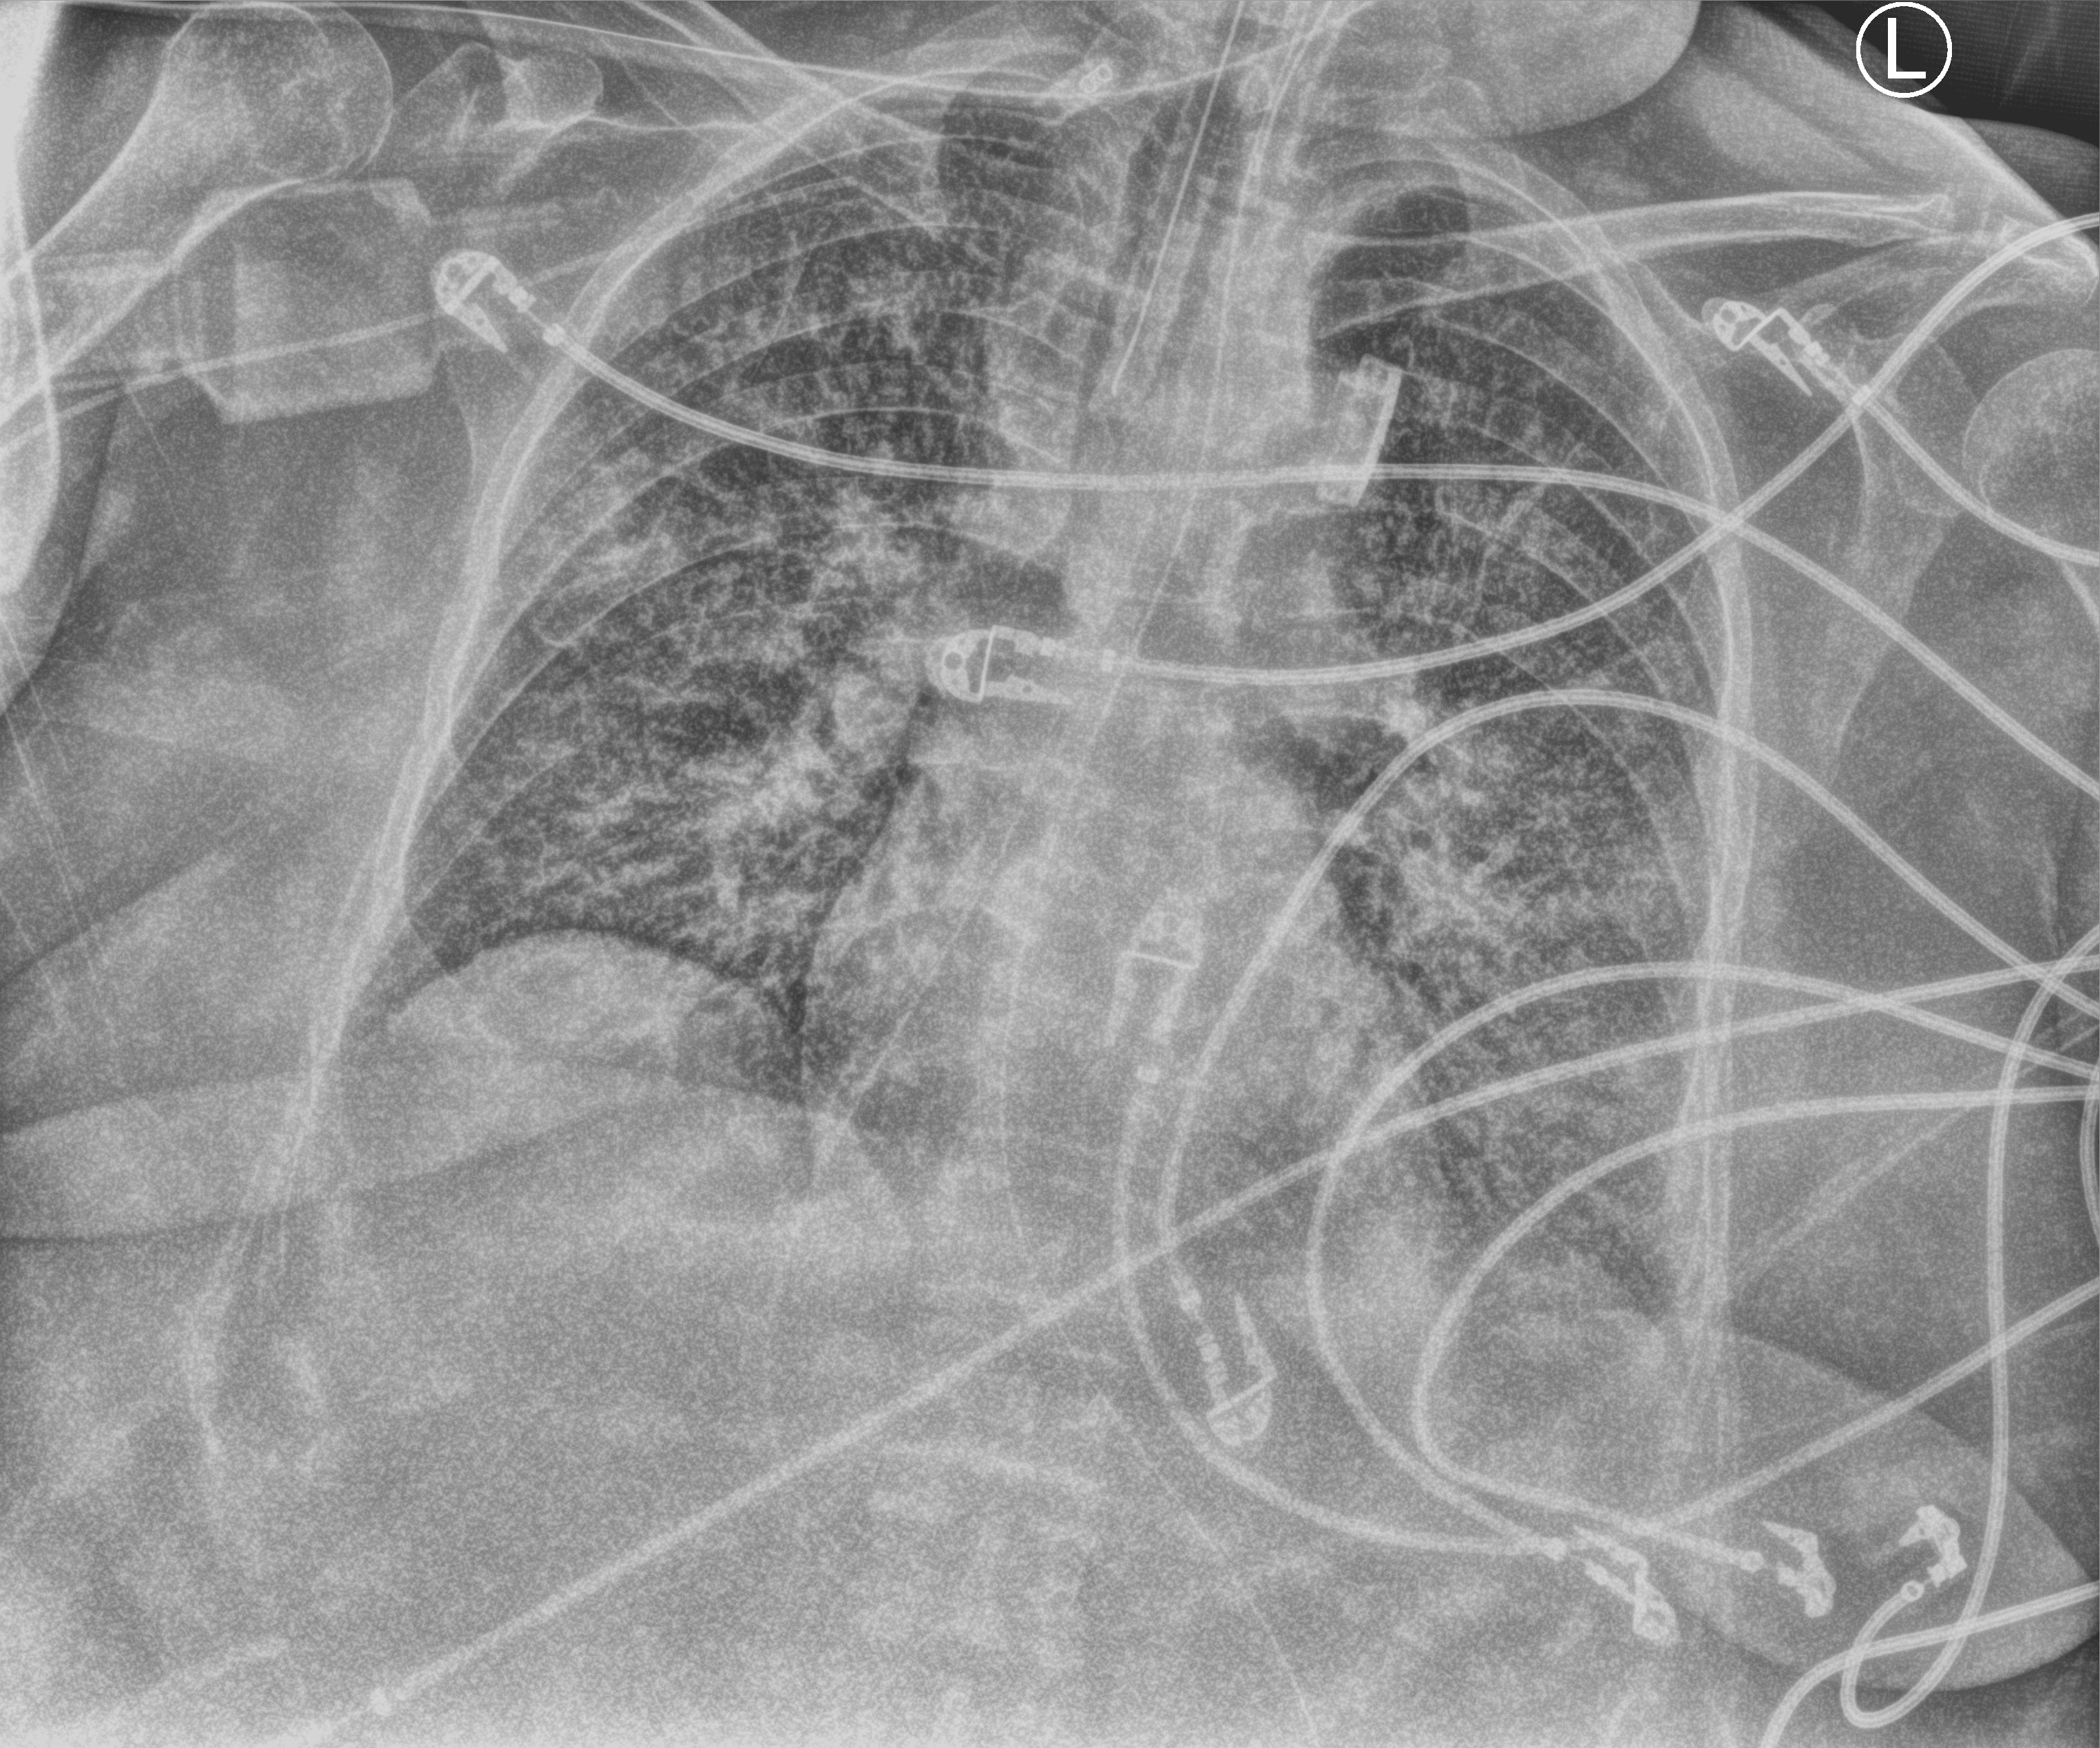
Chest X-ray (portable); anteroposterior (AP) projection. Patient hospitalised with COVID-19; female, aged 60–74 years.
From the hospital-stay record, not from the radiograph (when in the stay this image was taken is not recorded): admitted to intensive care during this hospital stay: yes; mechanically ventilated during this hospital stay: yes.